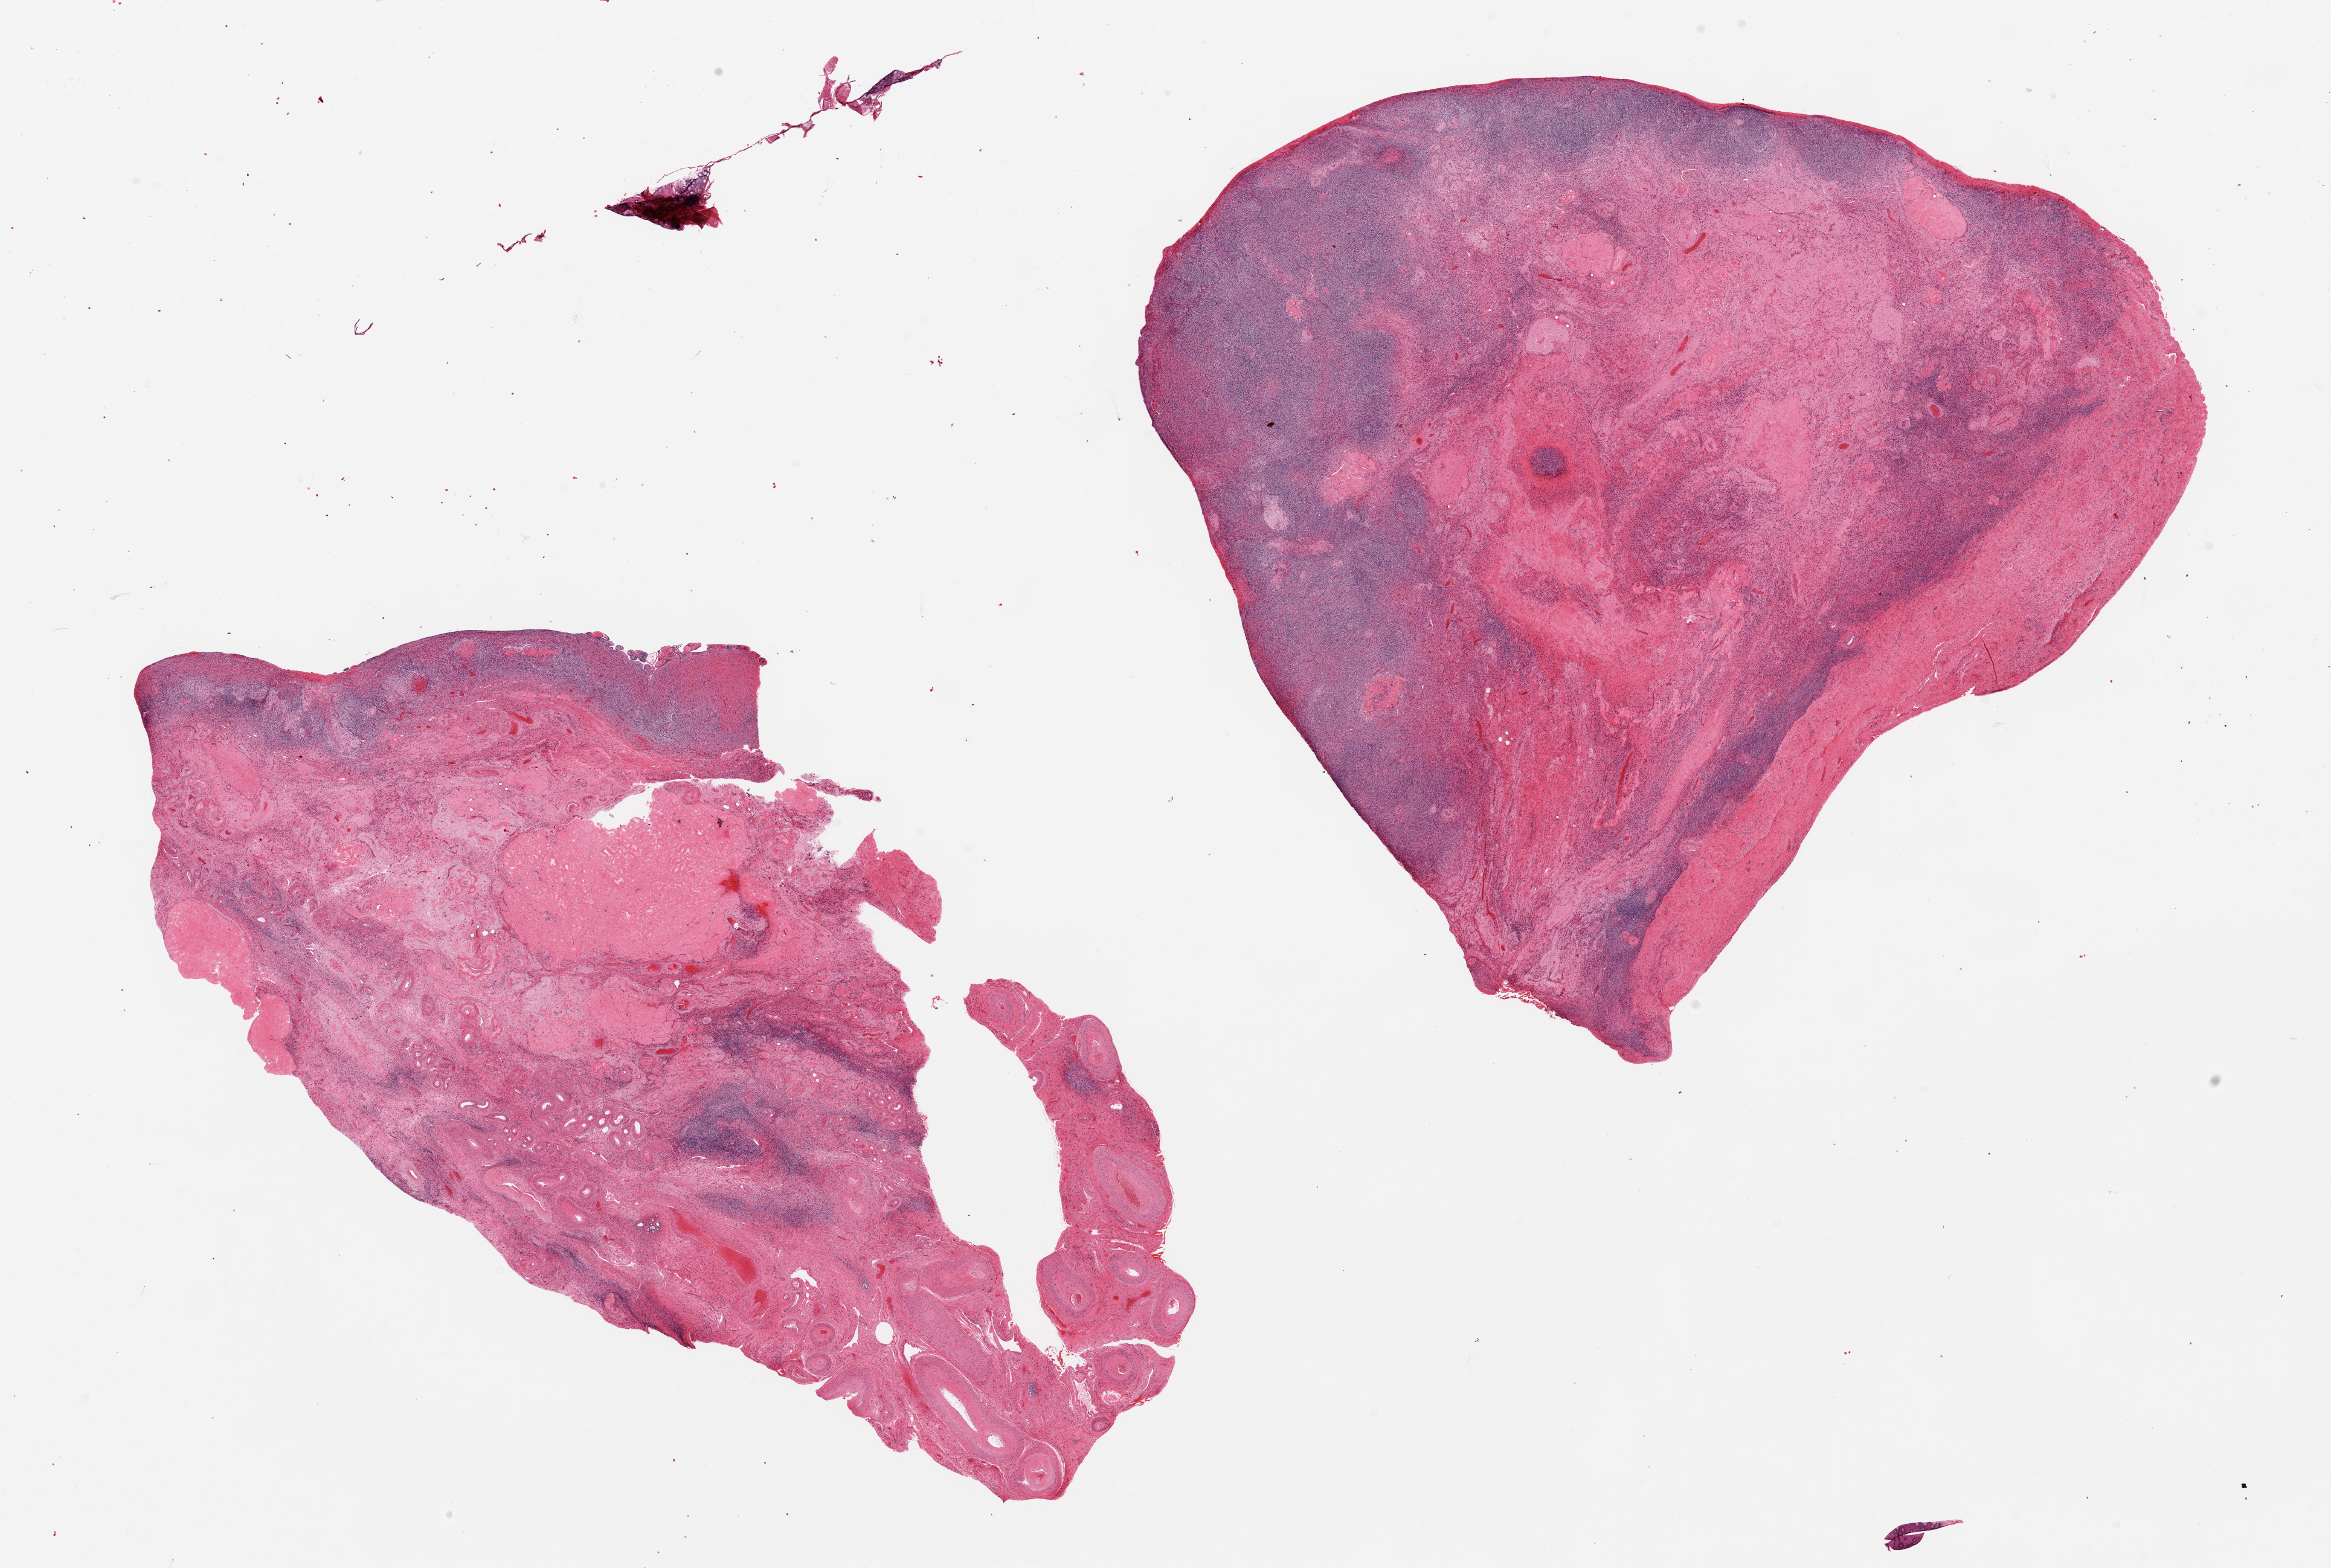
Digitized H&E-stained section, brightfield — whole scanned area (about 30.5 x 20.5 mm, acquisition: 20x scan) shown as a low-resolution overview. PAXgene-fixed paraffin-embedded (PFPE) section. Sampled site (target tissue): ovary. Tissue donor sample.
* review note (as recorded): 2 pieces, typical post menopausal atrophy